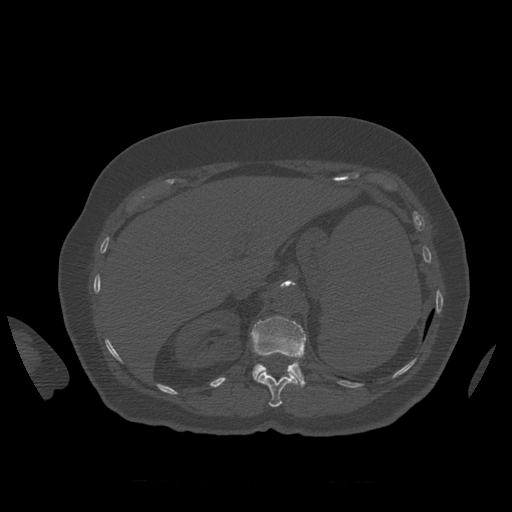
CT including the spine, one axial slice. Slice 290 of 399 in the series (ordered by position). Reconstruction kernel STANDARD. 120 kVp. Bone window (W 1800 / L 400 HU). 1.25 mm slice thickness. 512 × 512 image matrix, field of view 404 × 404 mm. Patient age 81 years. Case-level facts recorded for this patient, not image findings: primary cancer: renal.
Structures marked on this image (semi-automatically segmented with operator editing):
- L1 vertebra: bounding box [x1, y1, x2, y2] px = [251, 317, 307, 387]
- T12 vertebra: [256, 372, 297, 408]